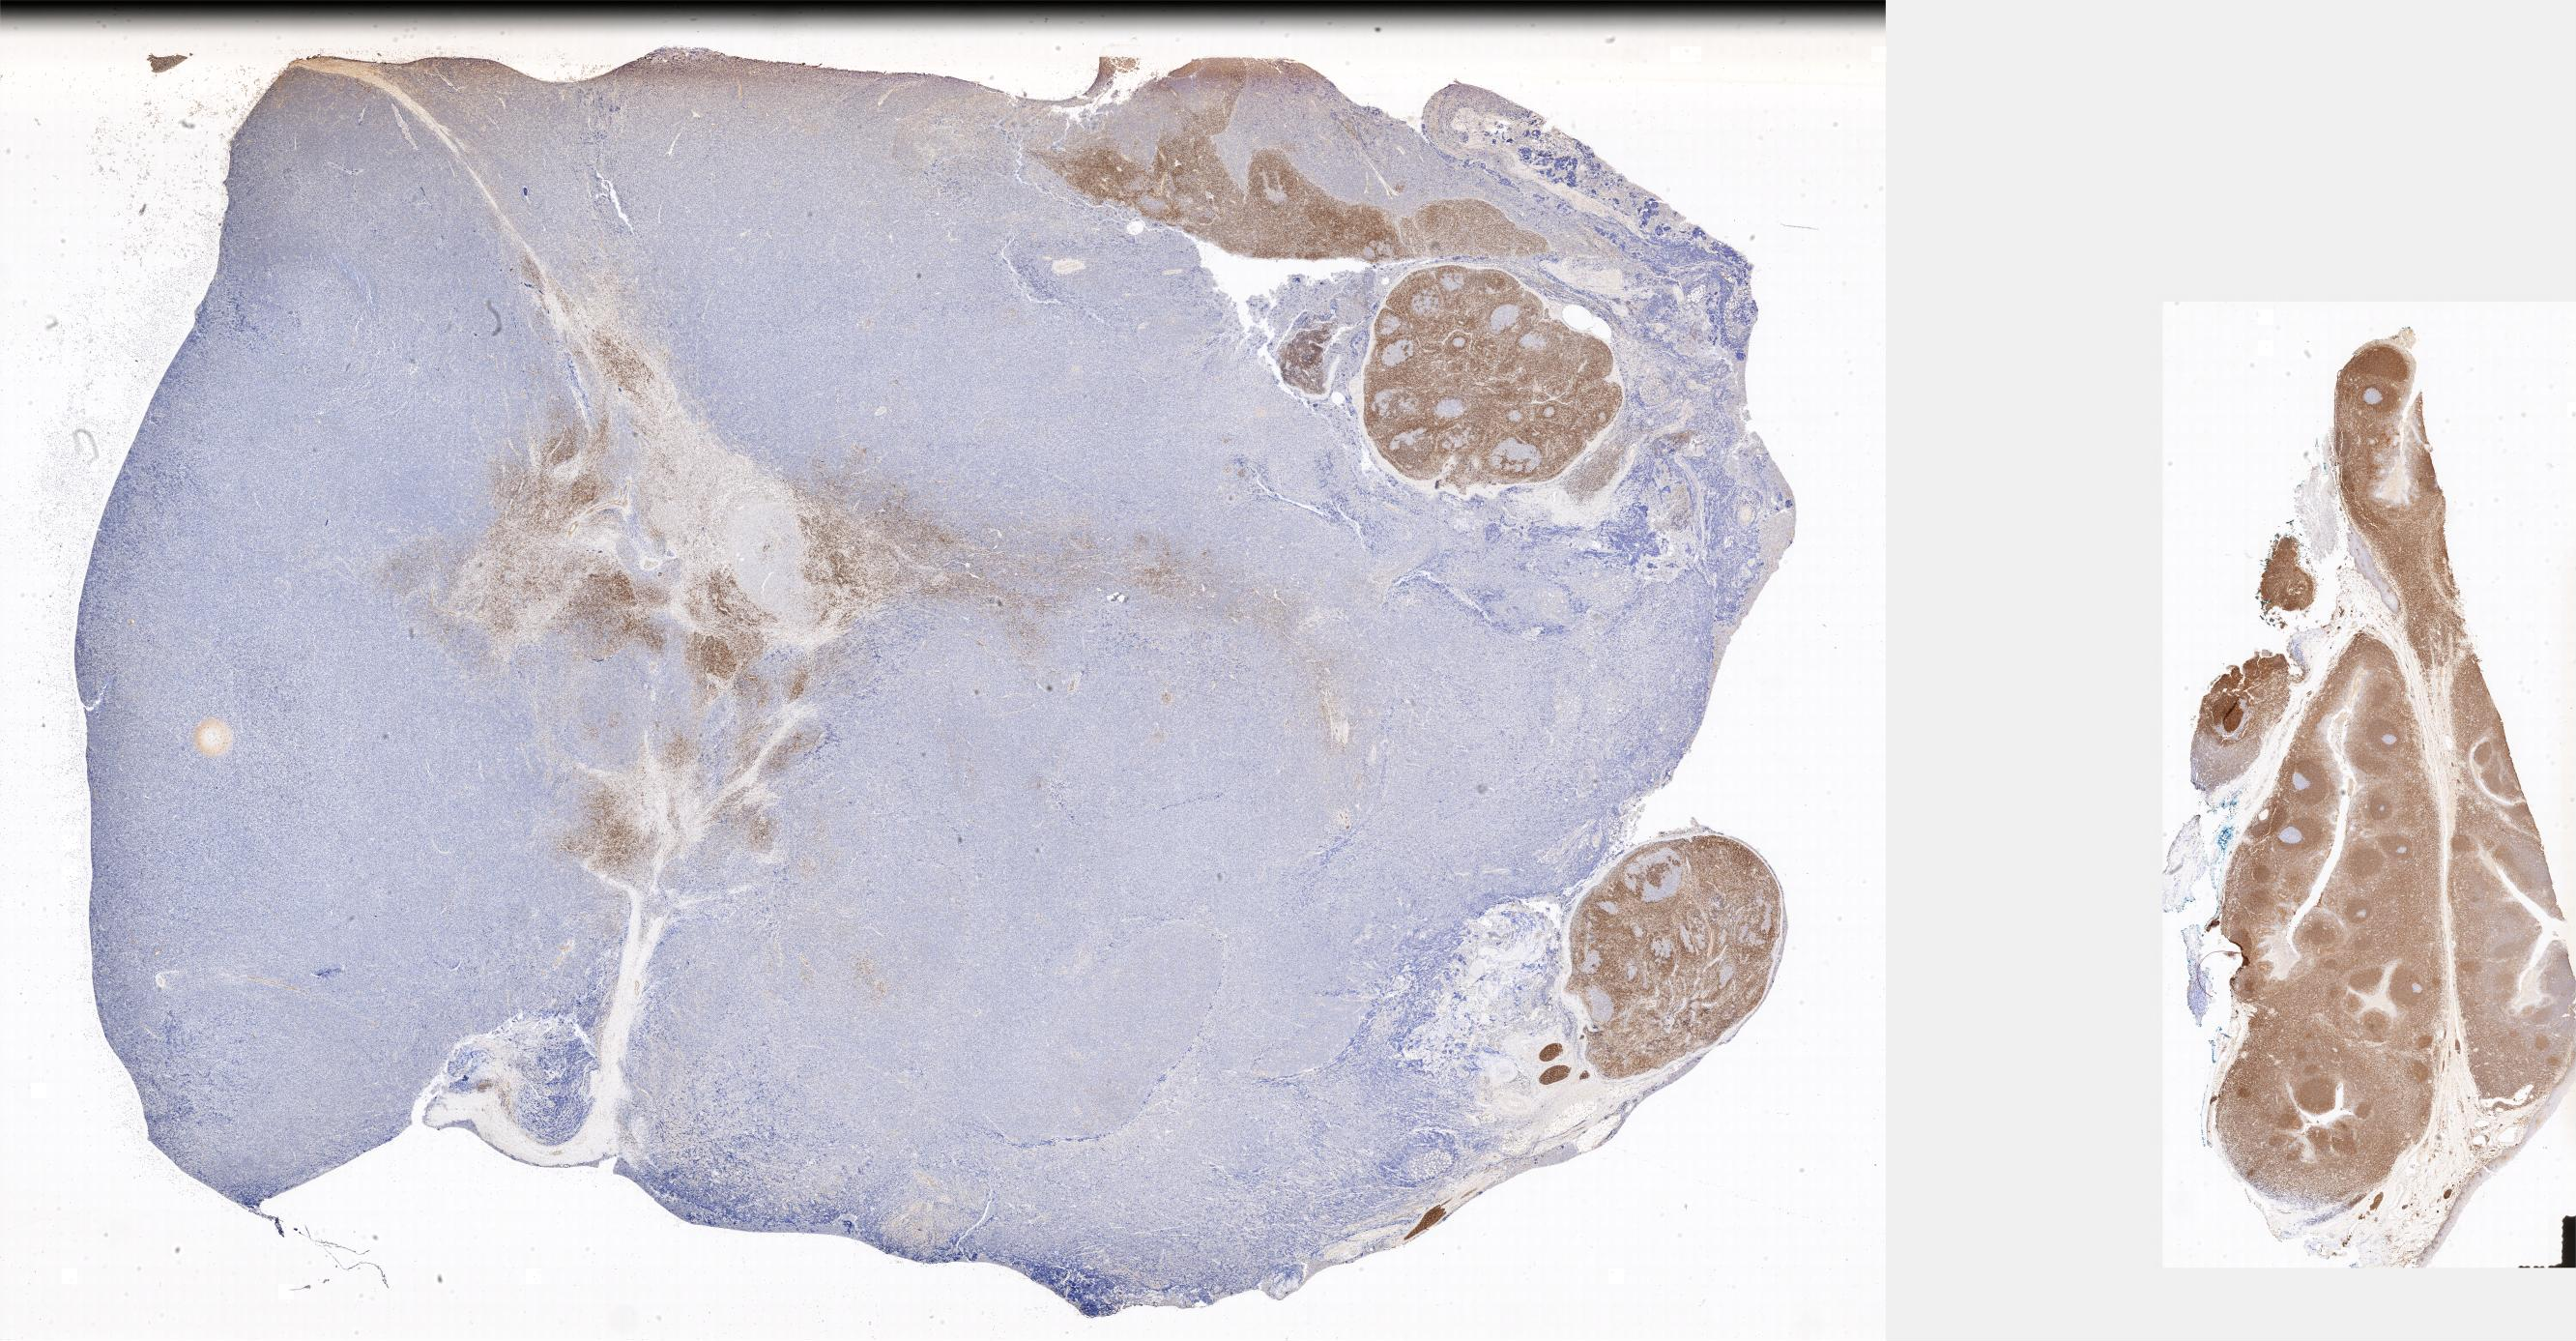
Whole-slide image, immunohistochemical stain for BCL2 — low-resolution overview of the scanned area. Specimen: tumor tissue. Site: lymph node of head and neck. Patient: male, age at initial diagnosis 3 years.
Histologic diagnosis: Burkitt lymphoma, NOS.